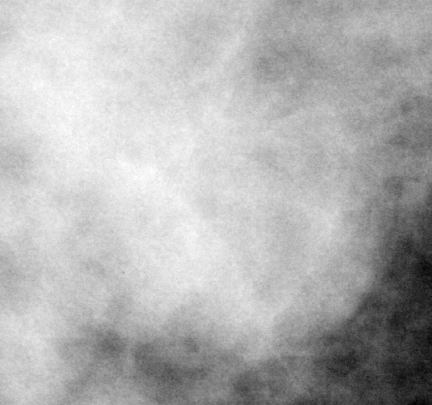
Region of interest cut from a scanned film mammogram (one marked finding); right breast; CC view; BI-RADS breast density category 3 (scale 1–4).
- Mass, shape lobulated, margins obscured; BI-RADS assessment category 3; pathology result (as recorded, not read from the image): benign.